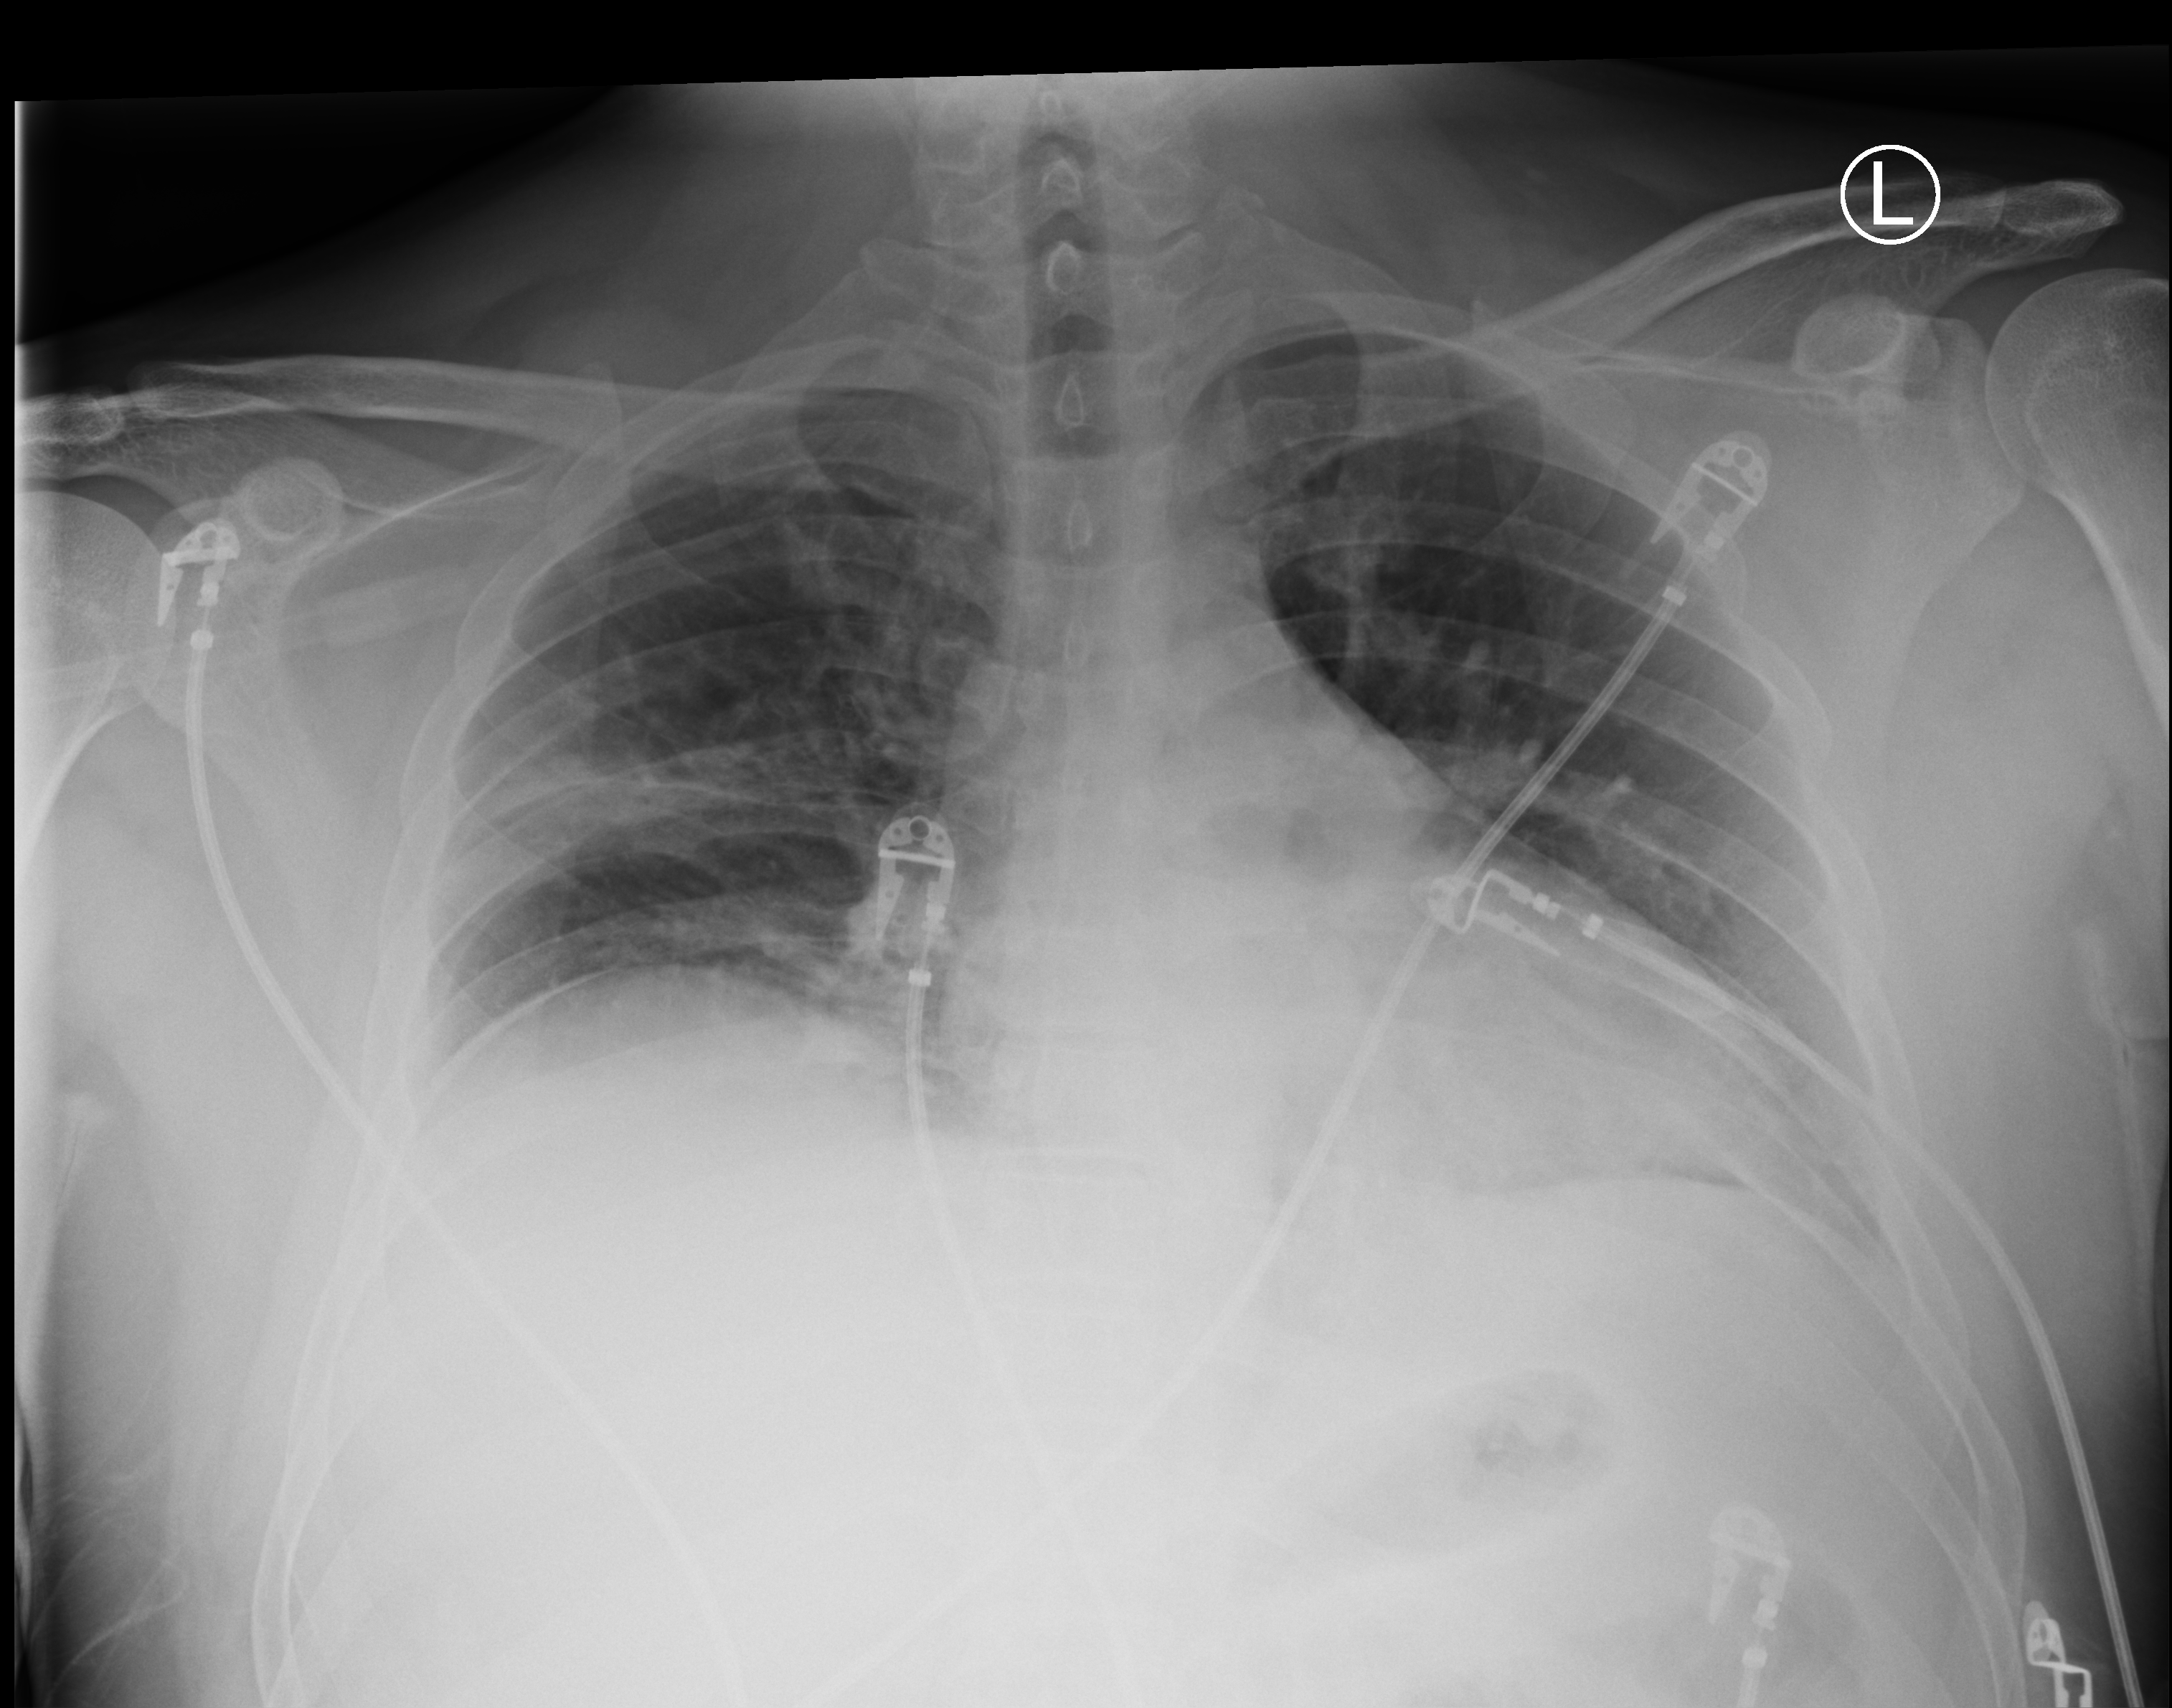
Chest X-ray (portable), anteroposterior (AP) projection. Adult patient hospitalised with COVID-19, age 18–59 years.
Hospital-stay facts (about this admission, not read from this image; timing relative to this image not recorded): admitted to intensive care during this hospital stay: yes; mechanically ventilated during this hospital stay: yes.